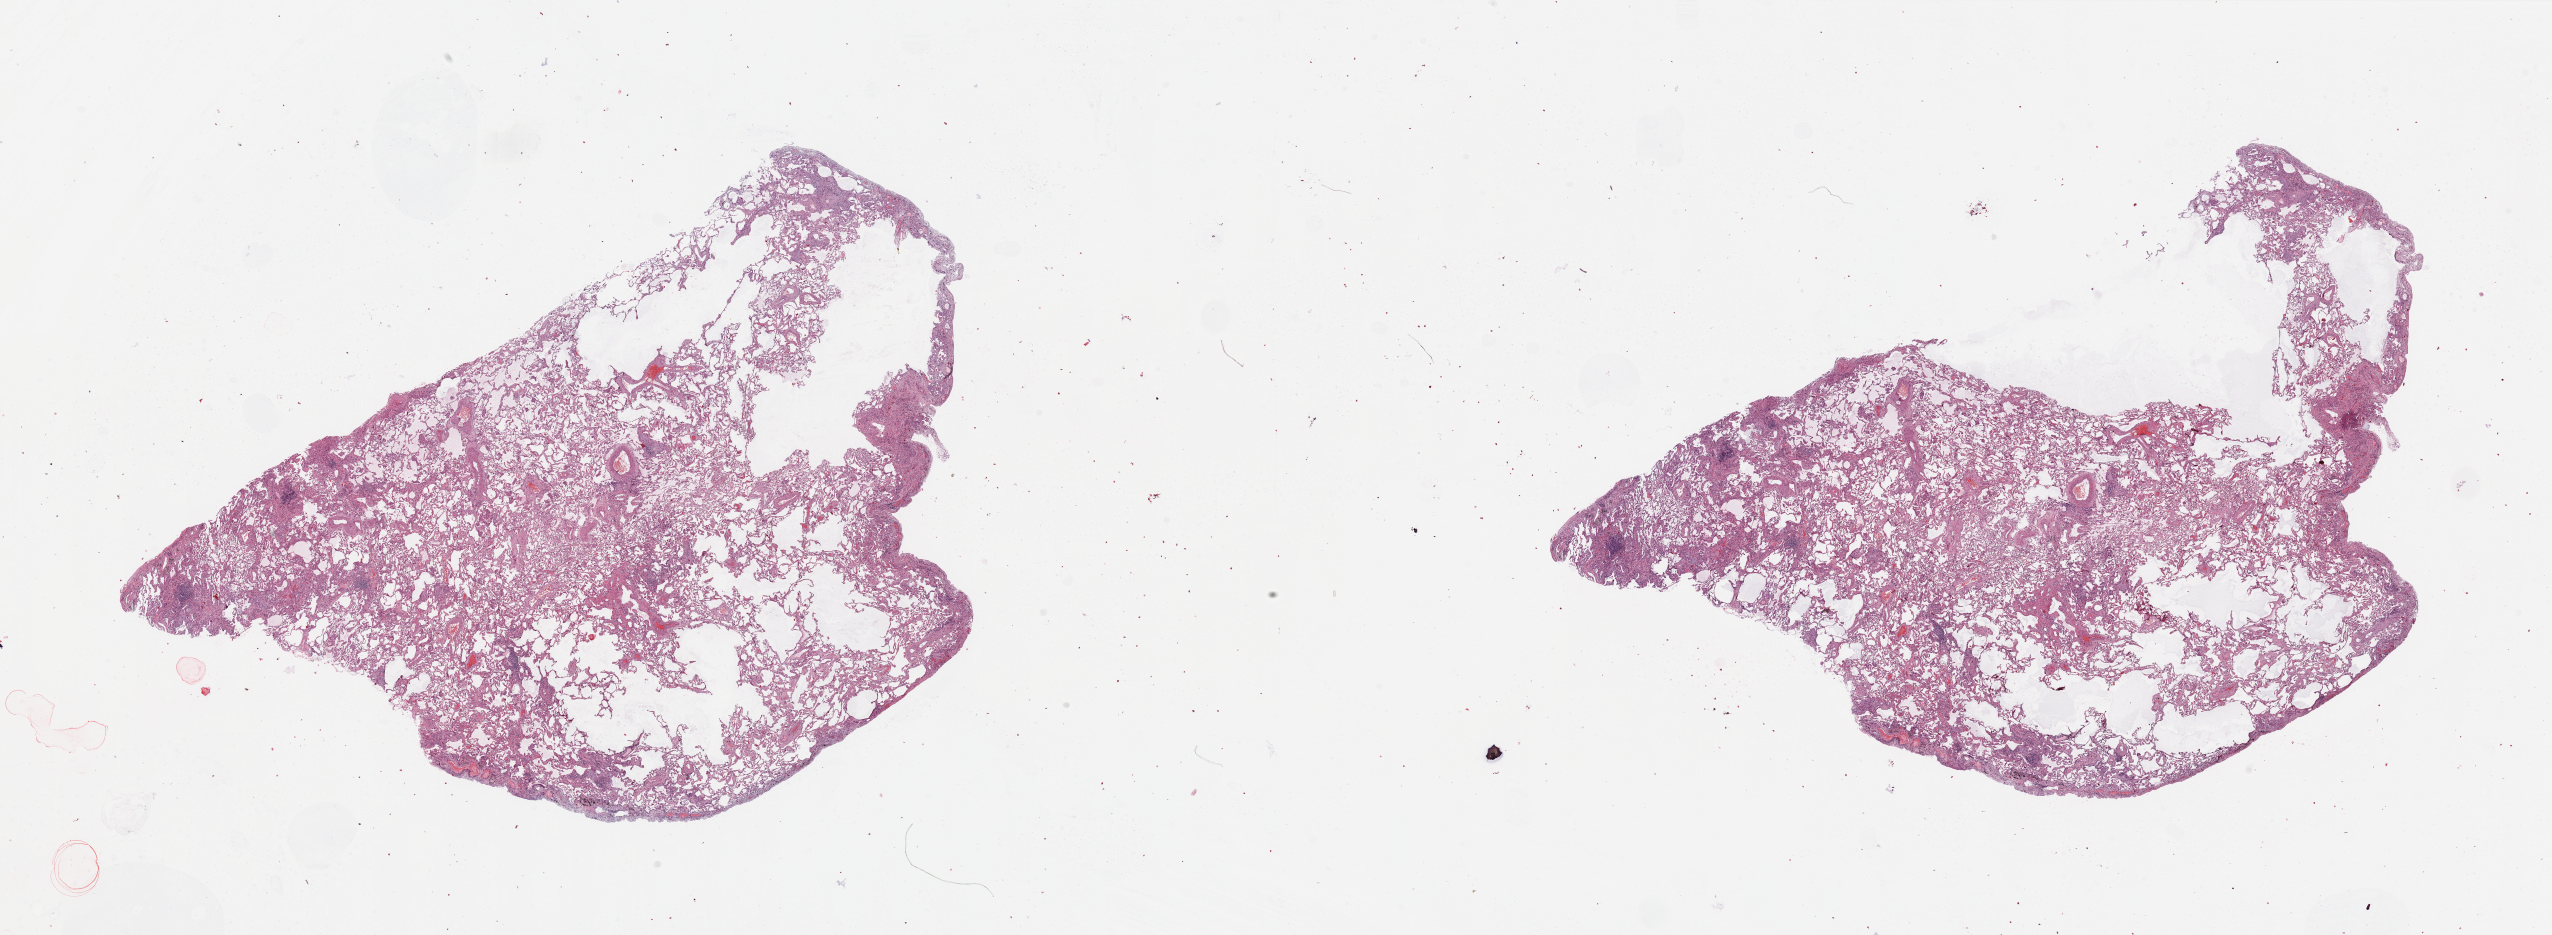
Whole-slide histology image, Hematoxylin and eosin (H&E) stained — a low-resolution overview of the entire scanned area, about 40.4 x 14.8 mm (acquisition: 20x scan); normal (non-tumour) tissue sample, sampled site: lung. 70-year-old male patient.
This section: normal (non-tumour) tissue from the same patient. Patient diagnosis: Squamous cell carcinoma, NOS.